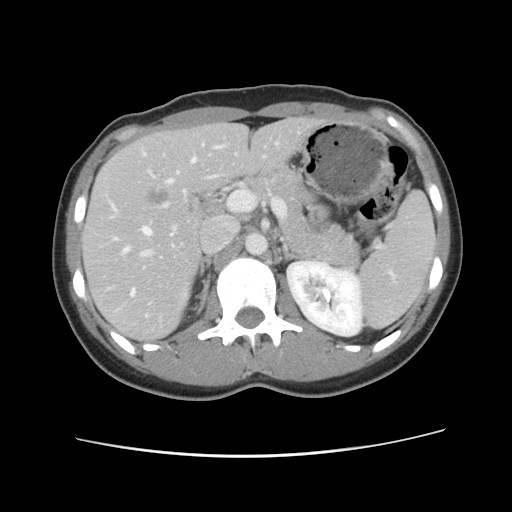
Contrast-enhanced abdominal CT, one axial slice; slice 61 of 134 in the series (ordered by position); 120 kVp; intravenous contrast given; soft-tissue window (W 400 / L 40 HU); 2.5 mm slice thickness; 512 × 512 image matrix, field of view 339 × 339 mm. Female patient, age 33 years. Case-level facts recorded for this patient, not image findings: diagnosis: colorectal cancer liver metastases, imaged before liver resection; multiple liver metastases: yes; largest metastasis: 4.5 cm; disease in both lobes: yes.
Structures marked on this image (manually delineated by an expert):
- hepatic veins: bounding box [x1, y1, x2, y2] px = [113, 143, 278, 317]
- liver: [84, 119, 319, 341]
- planned liver remnant (the part of the liver to remain after resection): [84, 118, 319, 340]
- portal vein (with intrahepatic branches): [138, 196, 235, 303]
- liver metastasis: [143, 183, 175, 209]